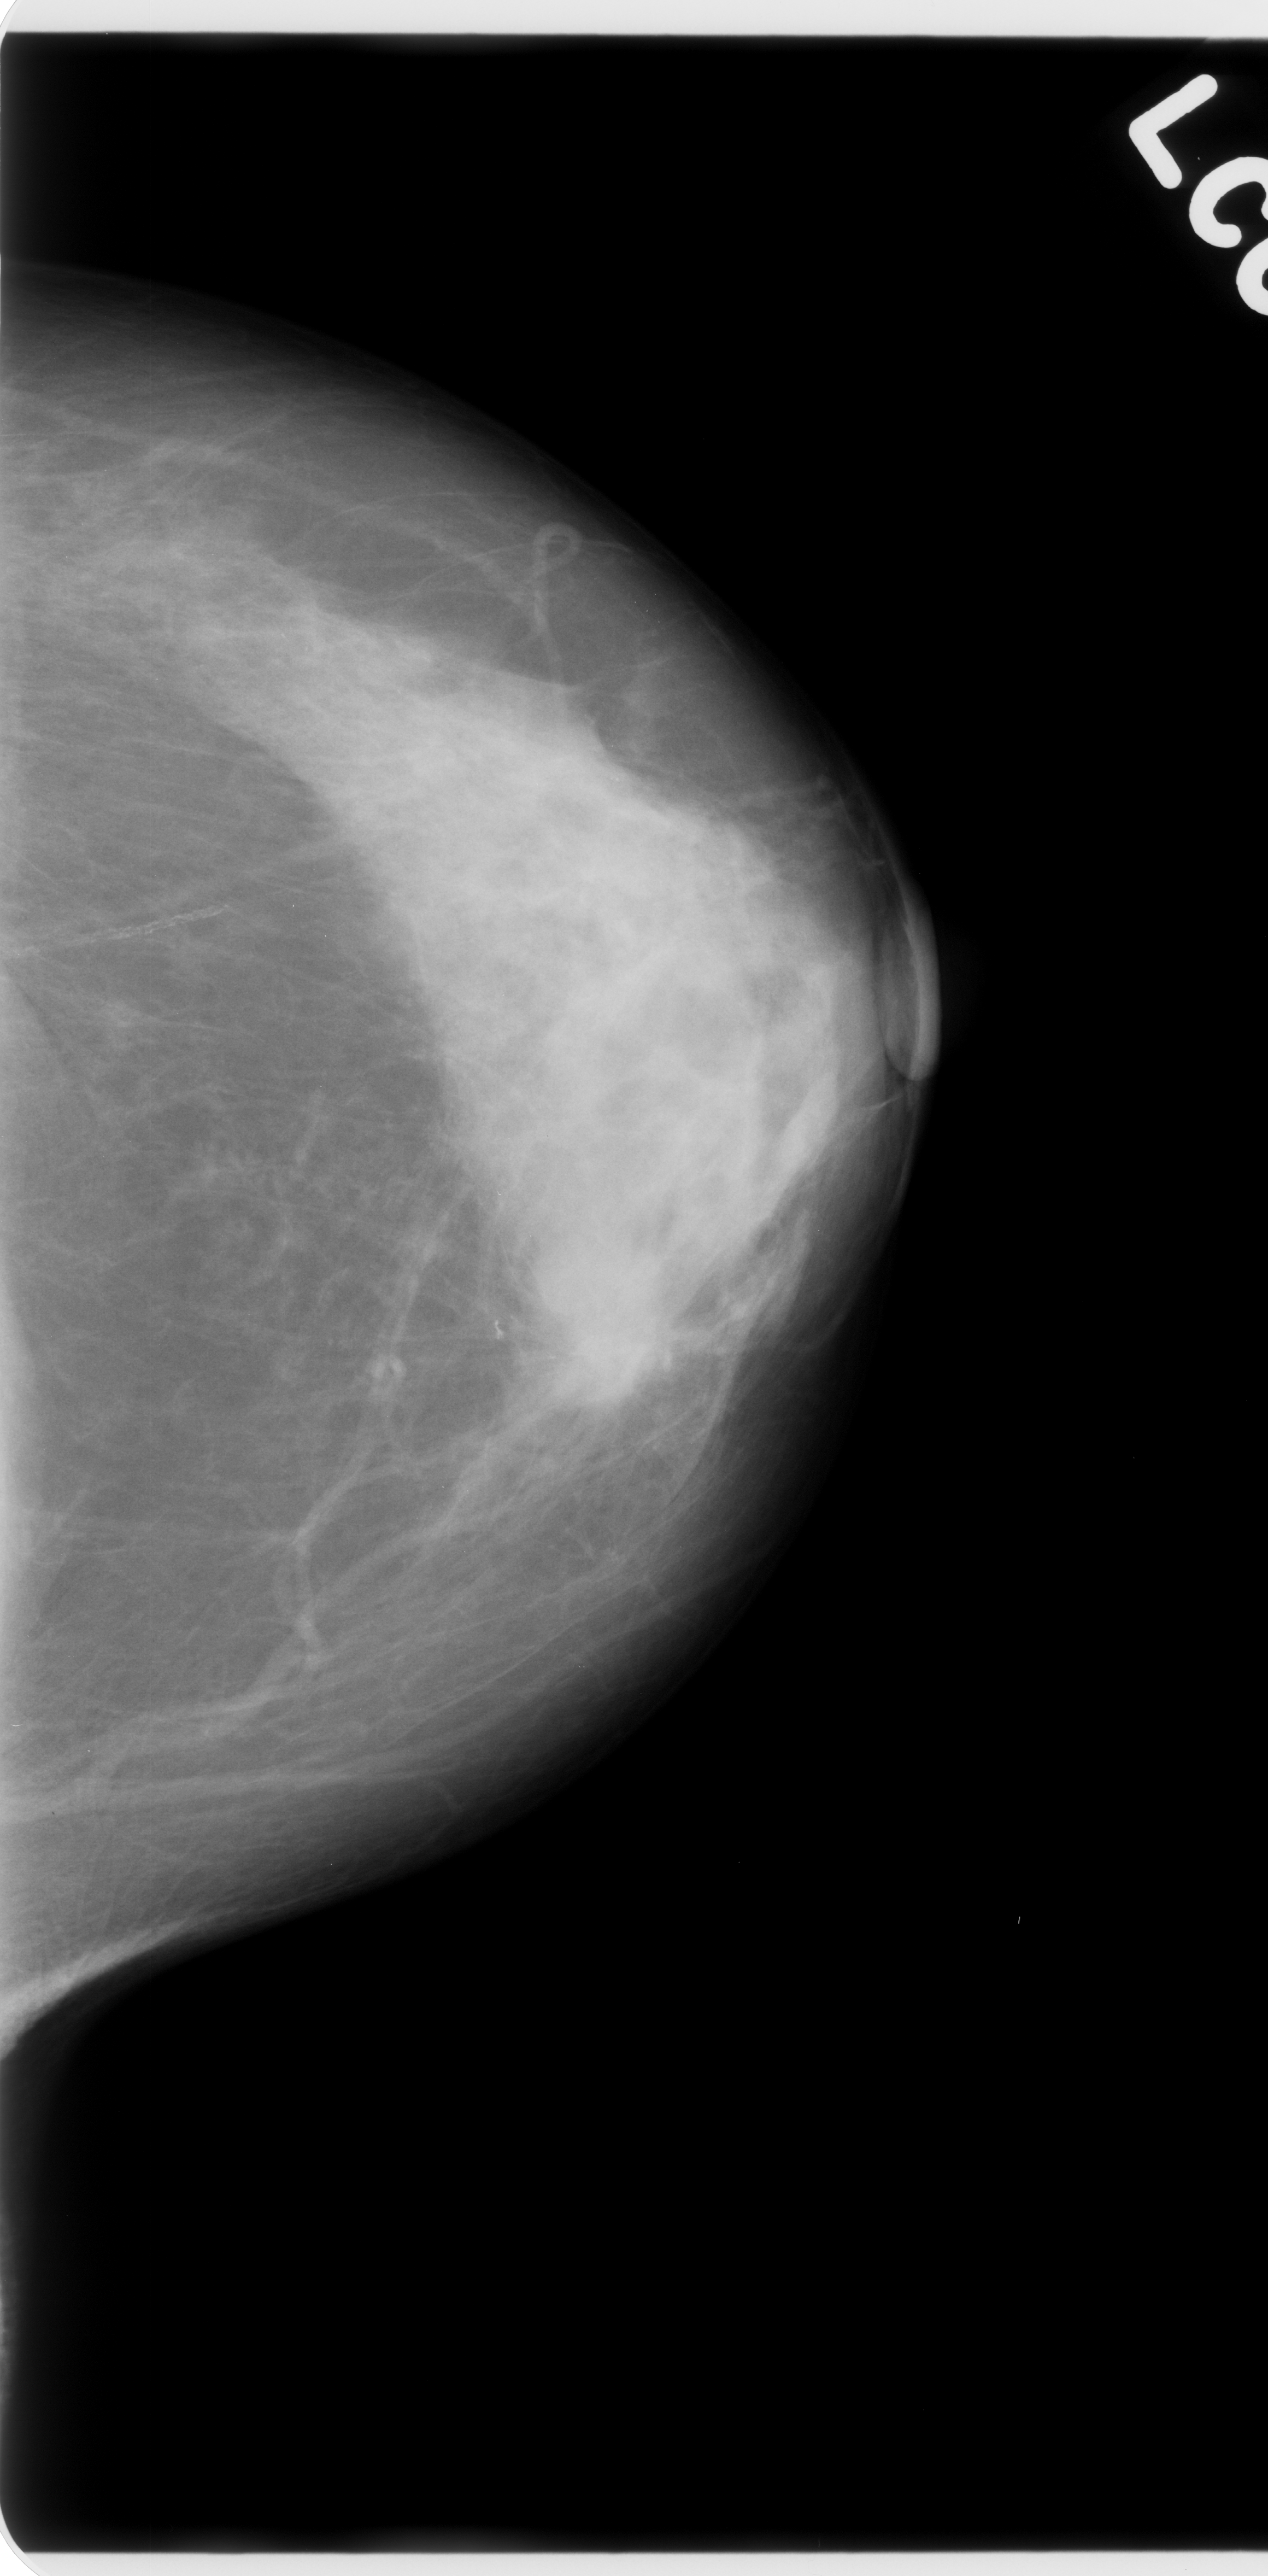
Digitized screen-film mammogram; left breast; craniocaudal (CC) view; breast composition: heterogeneously dense (BI-RADS density category 3 of 4).
Radiologist-marked abnormalities on this image: mass, shape lobulated, margins spiculated; BI-RADS assessment category 5; pathology (as recorded): malignant.